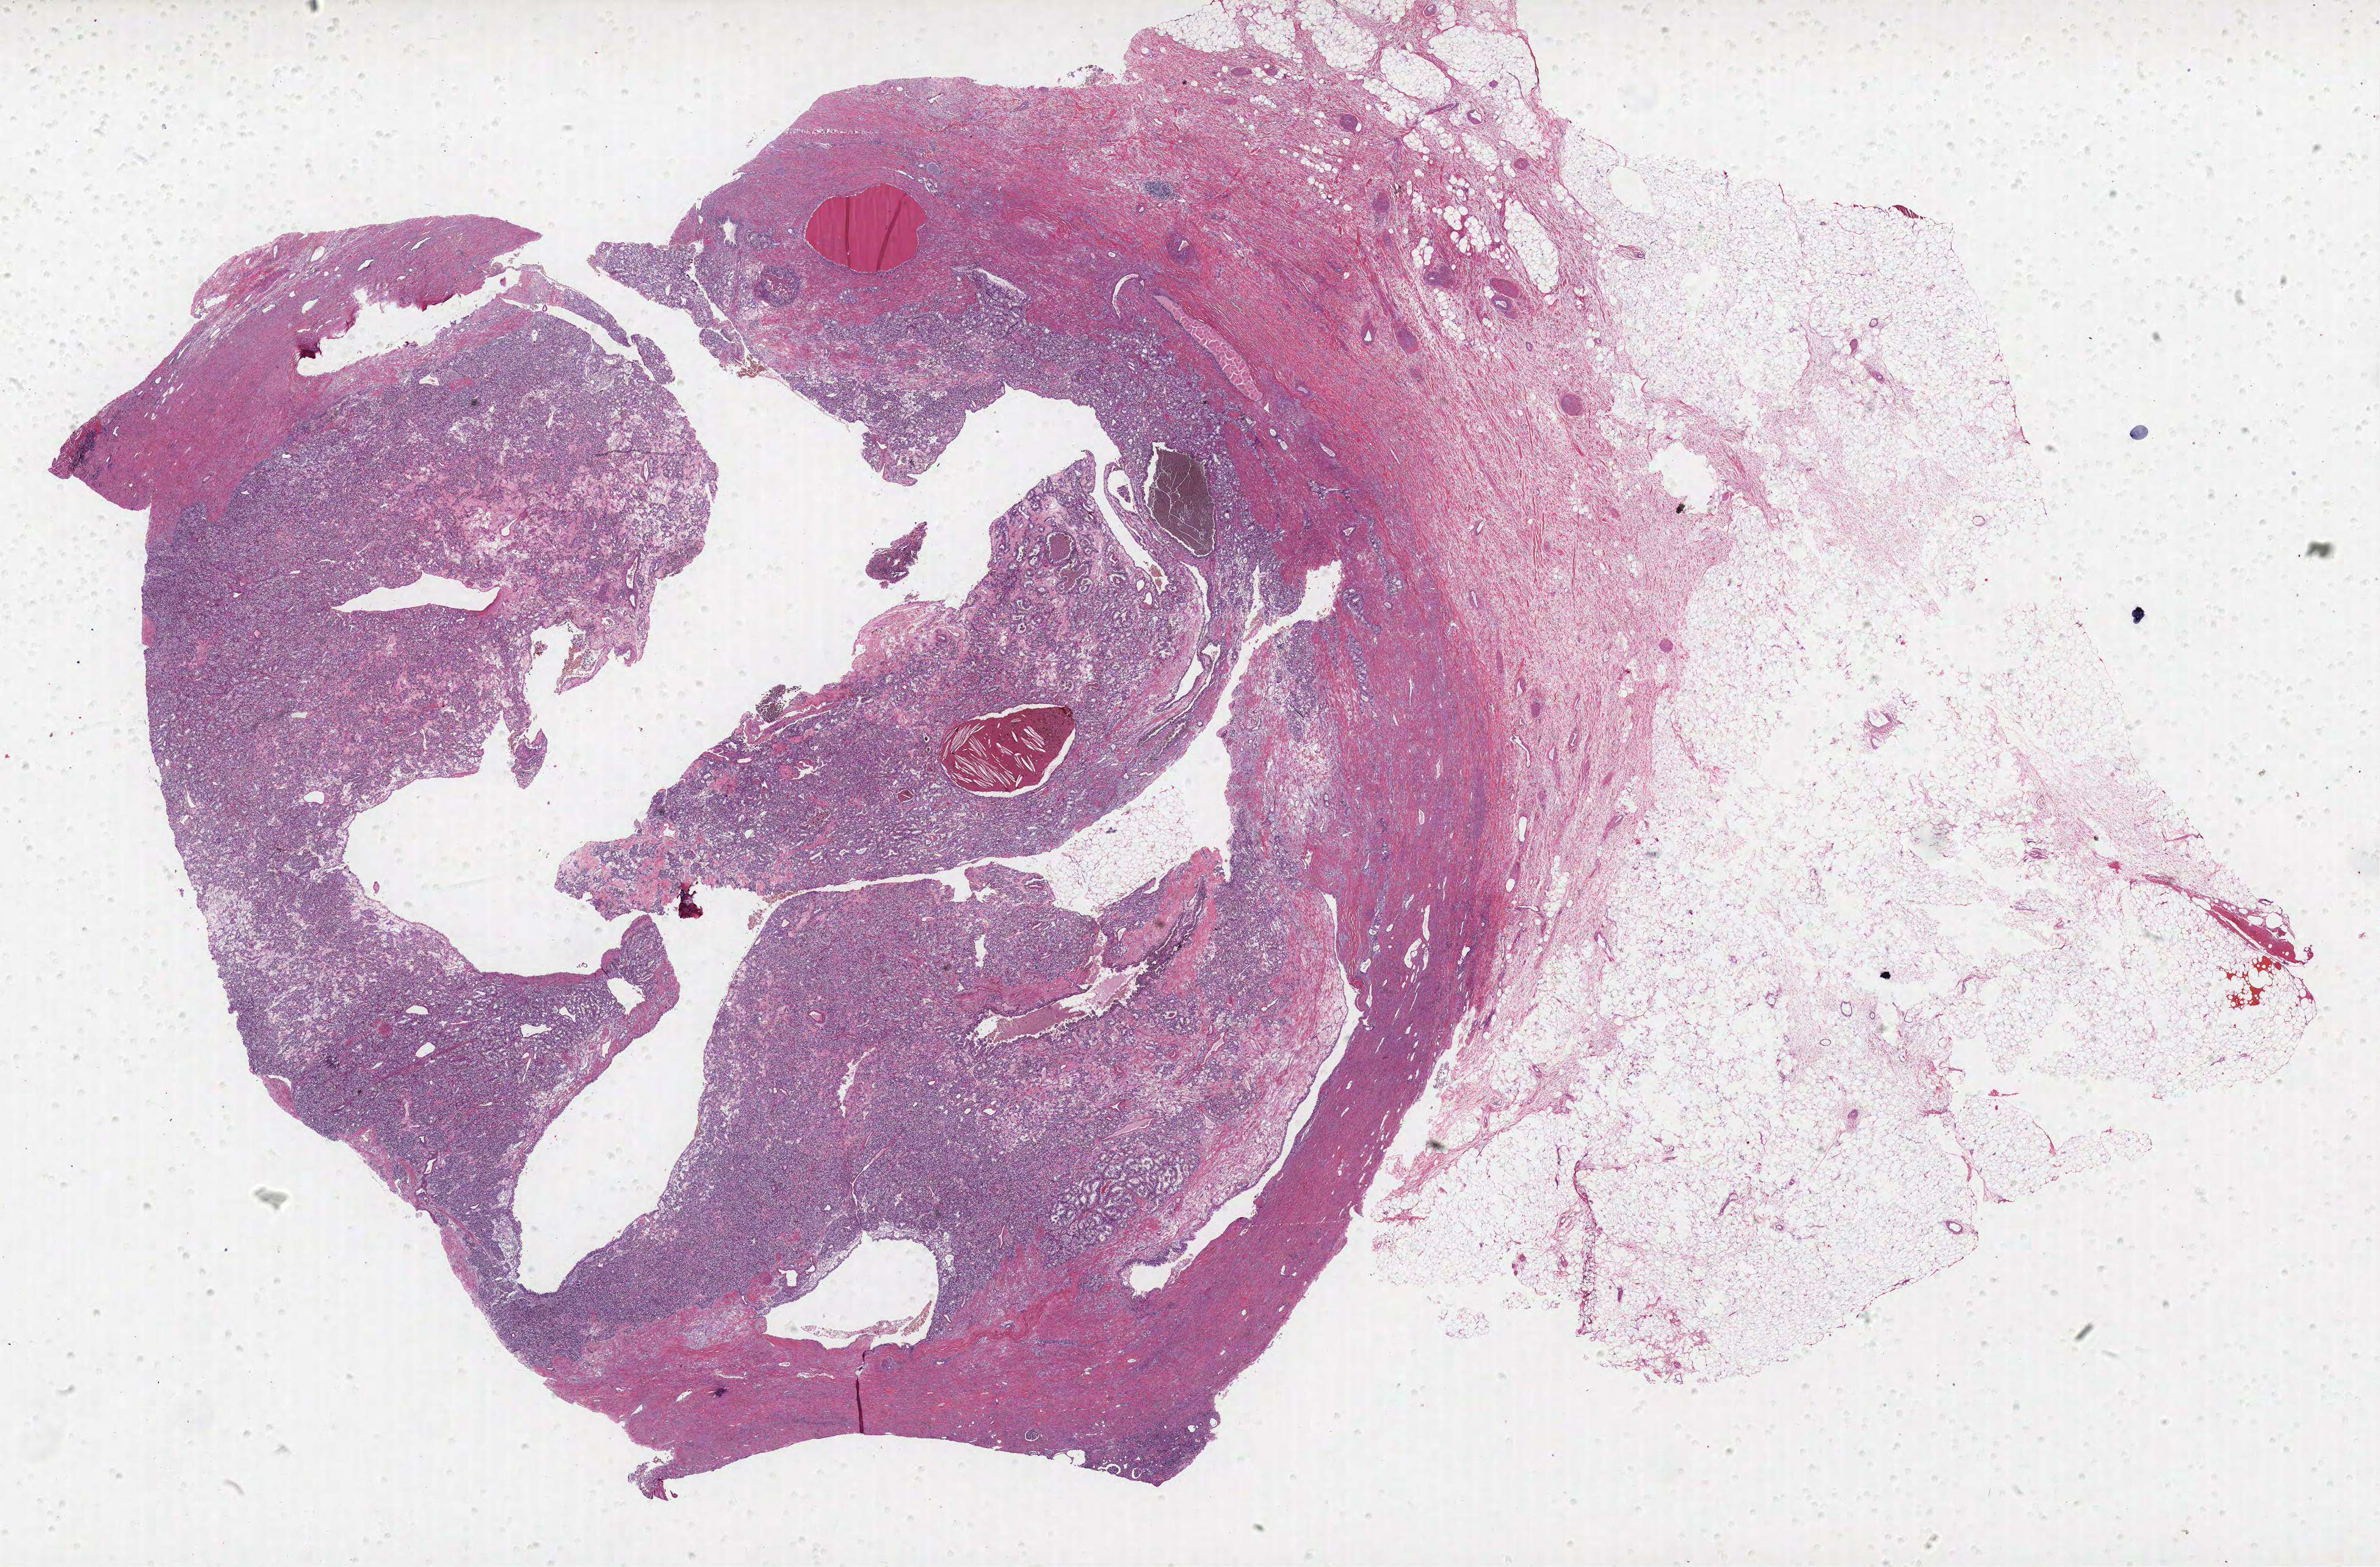
Digitized Hematoxylin and eosin (H&E) stained tissue section (whole slide), whole scanned area (about 31.2 x 20.5 mm) shown as a low-resolution overview. FFPE section. Primary tumour sample from the kidney. Male, age 63 years at initial diagnosis. Histologic grade: G2 (moderately differentiated).
- diagnosis: Clear cell adenocarcinoma, NOS
- AJCC pathologic stage: I